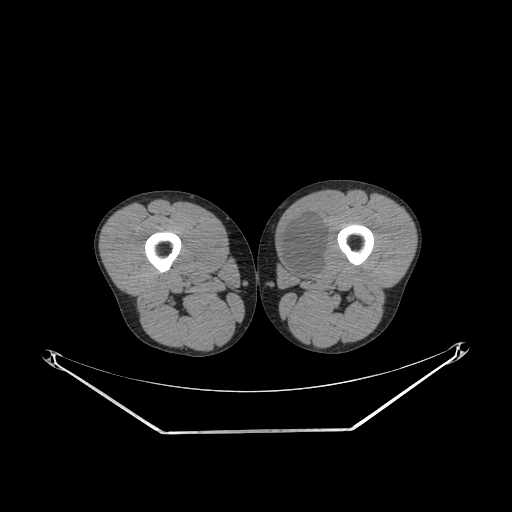
CT of an extremity soft-tissue mass (from a PET/CT study), one axial slice. Slice 239 of 311 in the series (ordered by position). Reconstruction kernel SOFT. Soft-tissue window (W 400 / L 40 HU). 3.75 mm slice thickness. 512 × 512 image matrix, field of view 500 × 500 mm. Male patient. From the clinical record (not read from this slice): histological type: mixoid liposarcoma; grade: low; site of the primary tumour: left thigh.
Outlined on this slice (expert contour drawn on MRI and transferred to this co-registered scan by the dataset authors):
- gross tumour volume (mass): bounding box <281,215,328,277> (left, top, right, bottom; pixels)